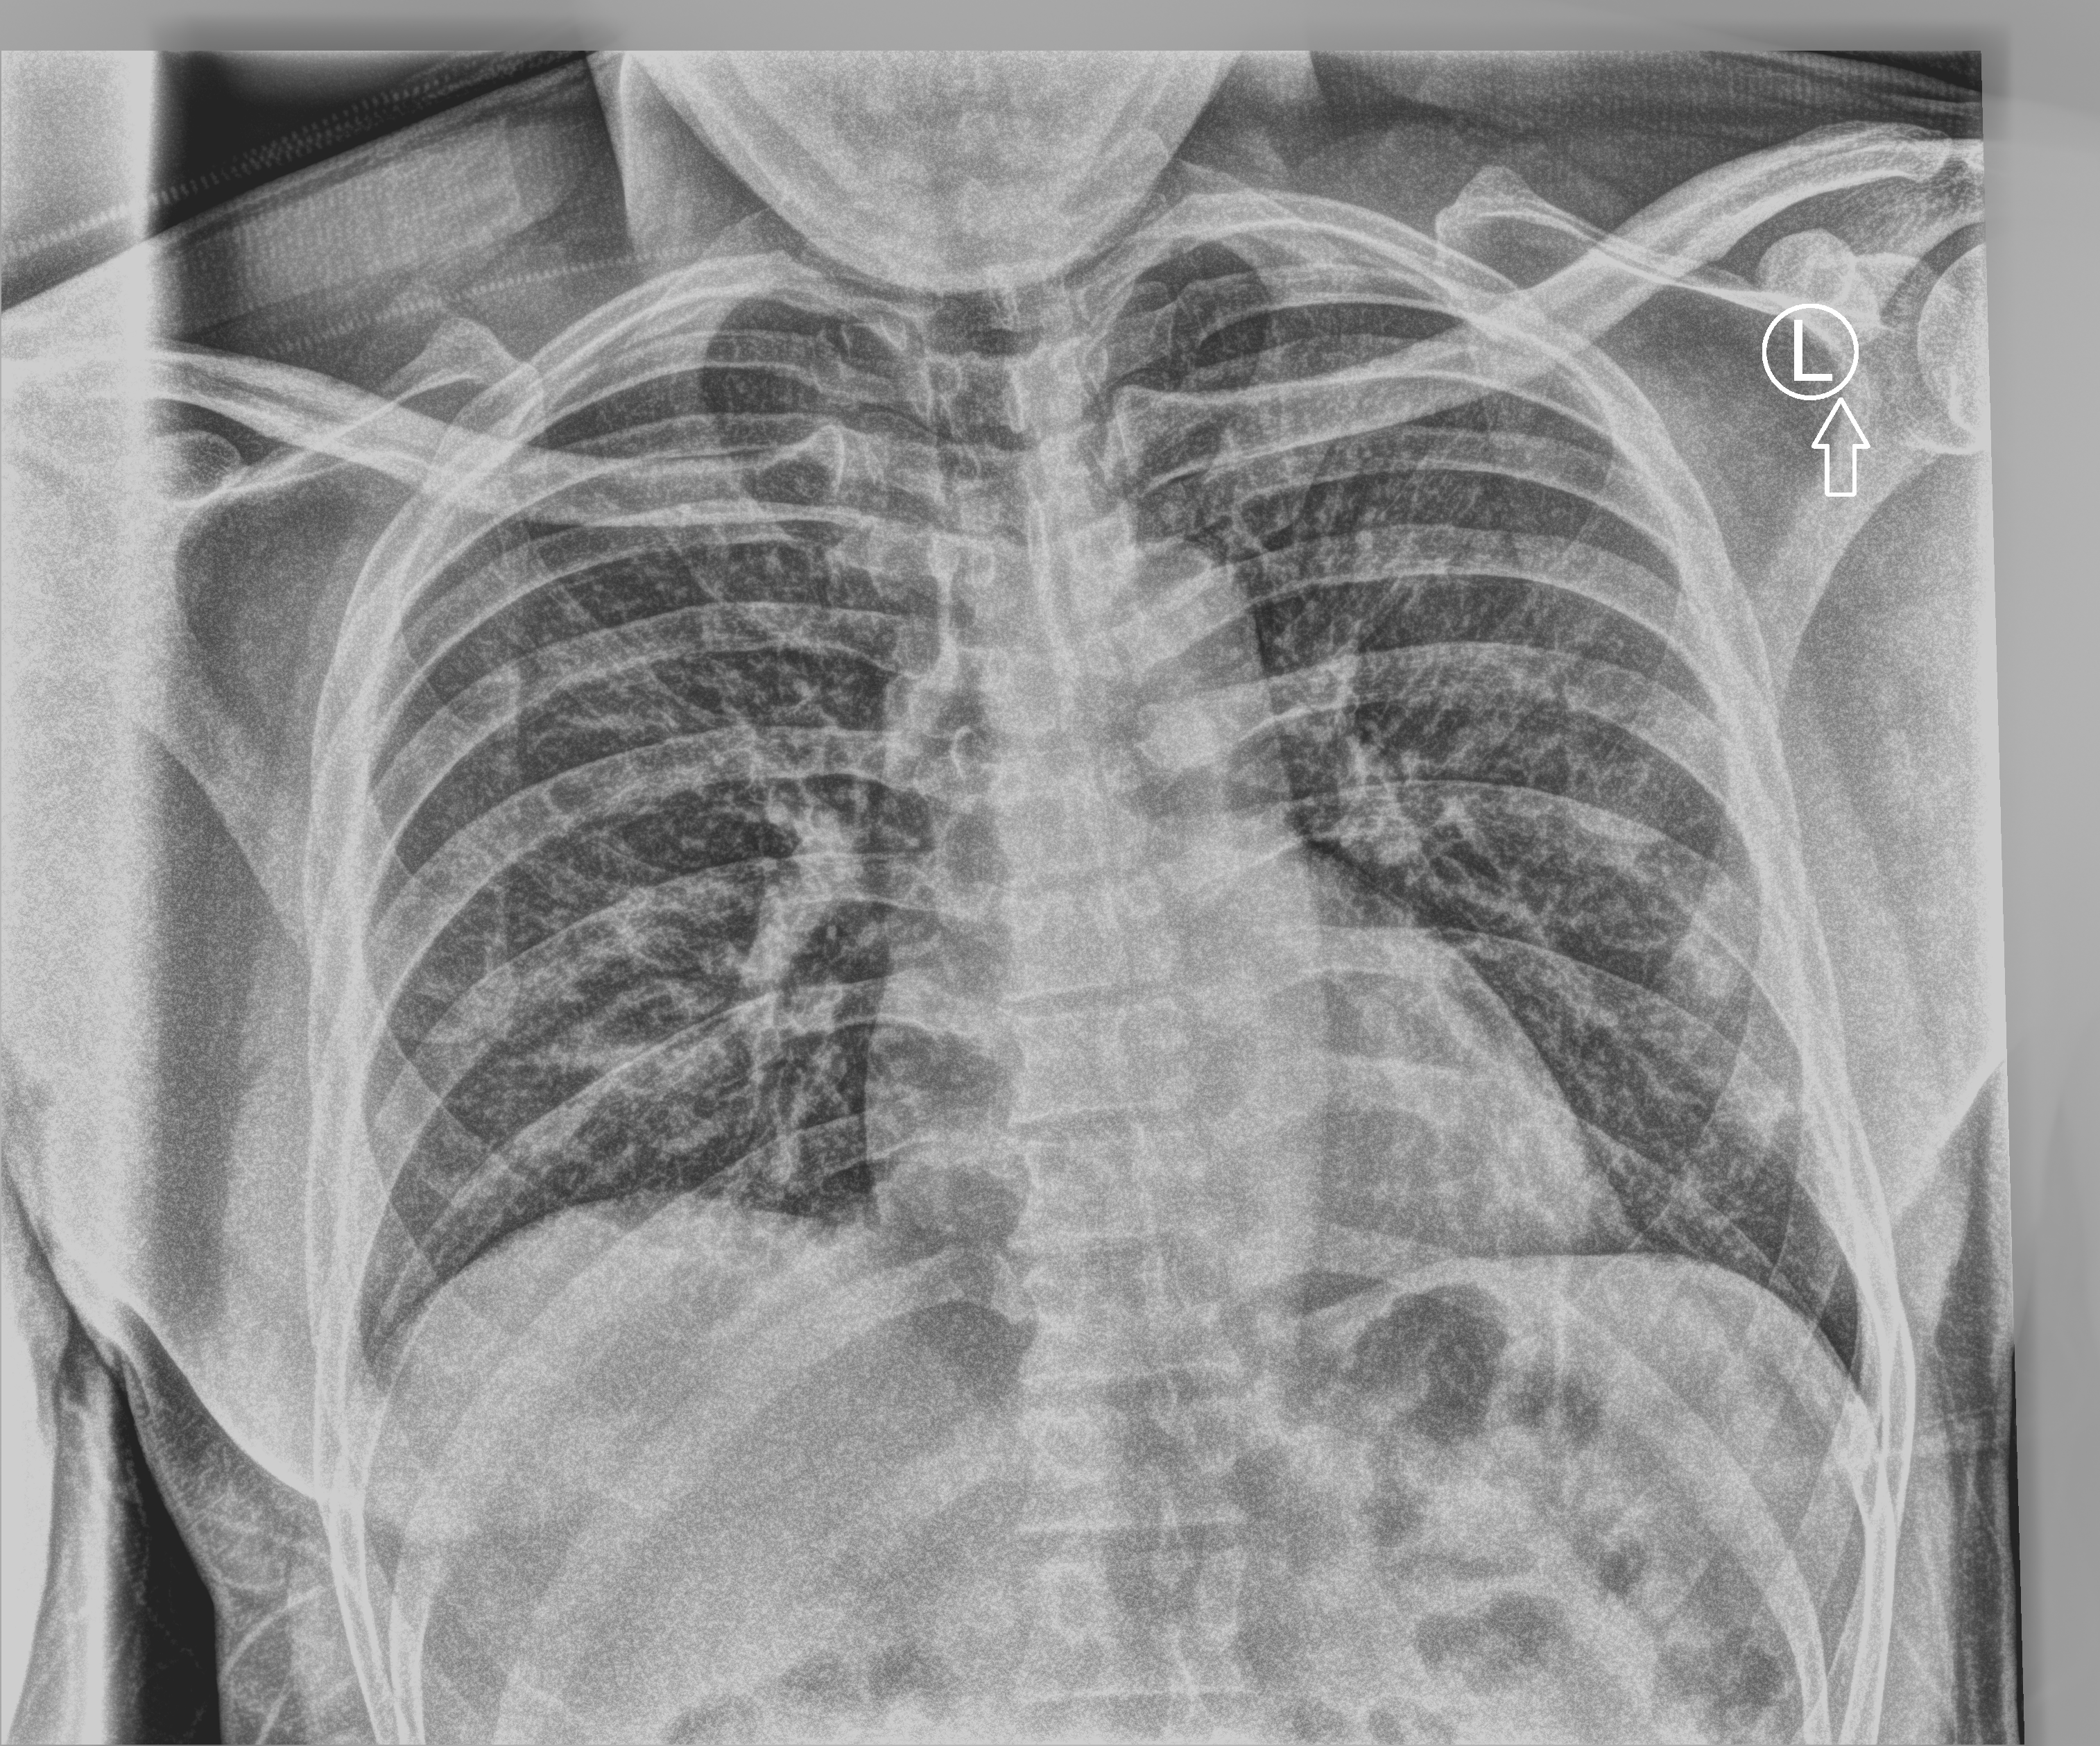
Portable chest radiograph. Patient hospitalised with COVID-19; male, aged 18–59 years.
Hospital-stay facts (about this admission, not read from this image; timing relative to this image not recorded):
- length of hospital stay: 2 days
- mechanically ventilated during this hospital stay: no
- admitted to intensive care during this hospital stay: no